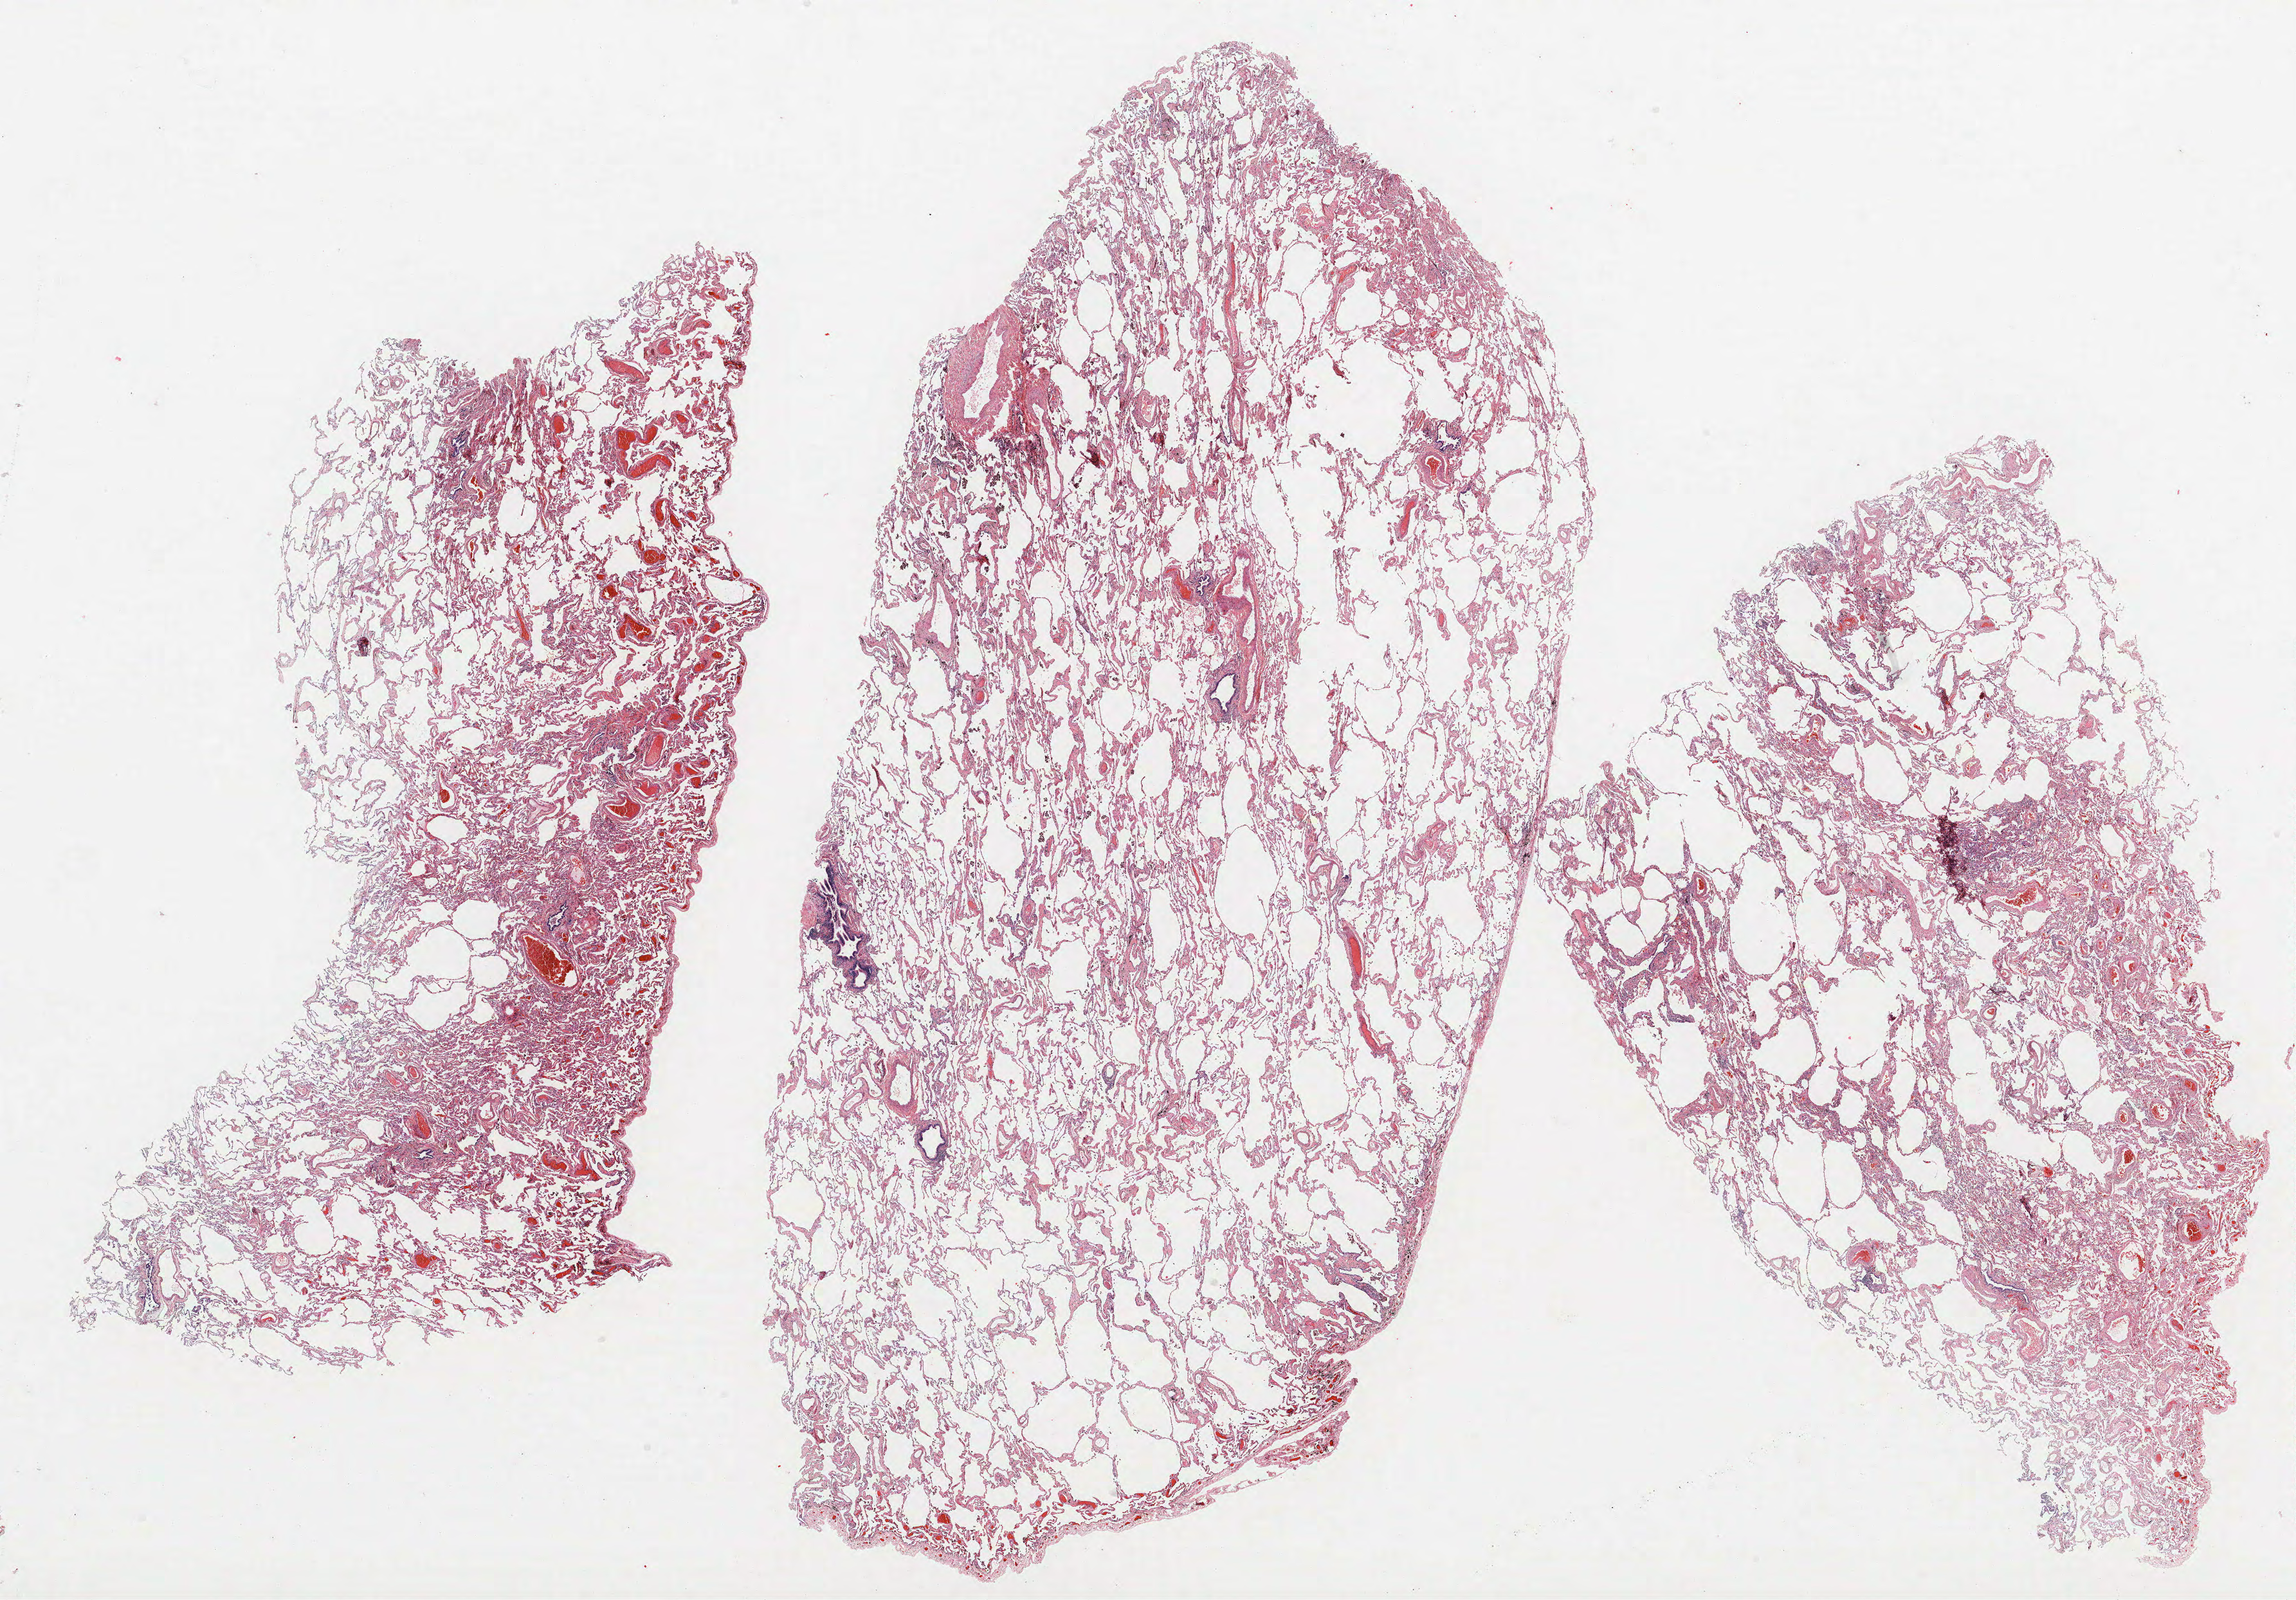
H&E whole-slide image, a low-resolution overview of the entire scanned area, about 28.6 x 19.9 mm. Formalin-fixed paraffin-embedded (FFPE) section. Lung tissue. Female, age 59 at enrolment. Current smoker at enrolment.
Participant's lung-cancer diagnosis: Adenocarcinoma, NOS.